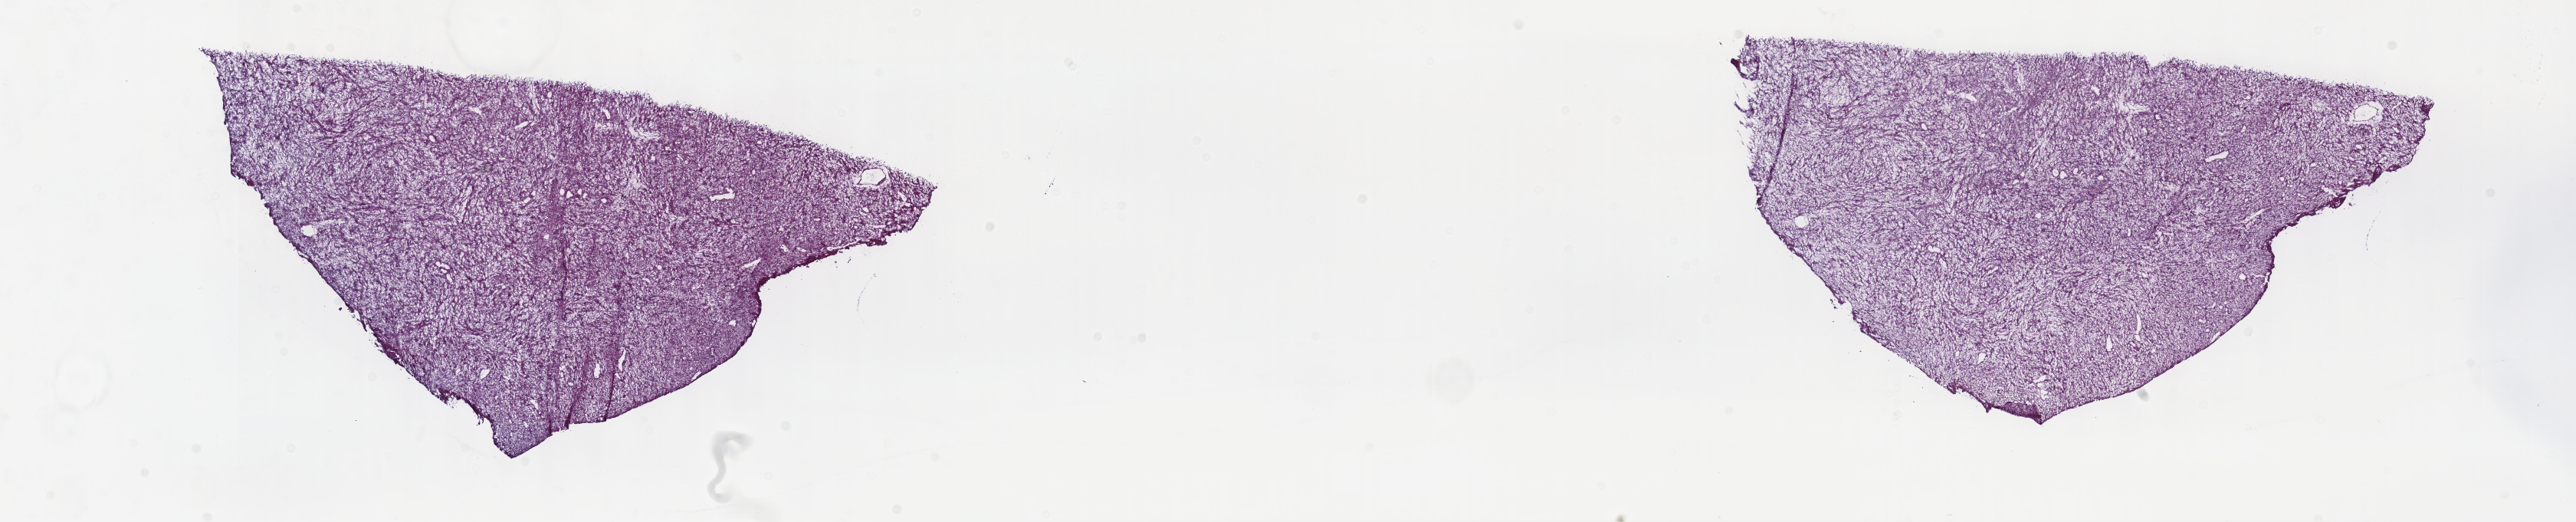
H&E whole-slide image — a low-resolution overview of the entire scanned area, about 27.2 x 5.5 mm; frozen section from the top of the tissue portion; retroperitoneum and peritoneum, primary tumour sample. Female patient; age at initial diagnosis 53 years. Slide review estimates, as recorded: tumour cells 100%, tumour nuclei 80%, normal cells 0%, stromal cells 0%, necrosis 0%. Infiltration values recorded for this section: lymphocyte infiltration 1%, monocyte infiltration 0%, neutrophil infiltration 0%.
Histologic diagnosis: Leiomyosarcoma, NOS (retroperitoneum).